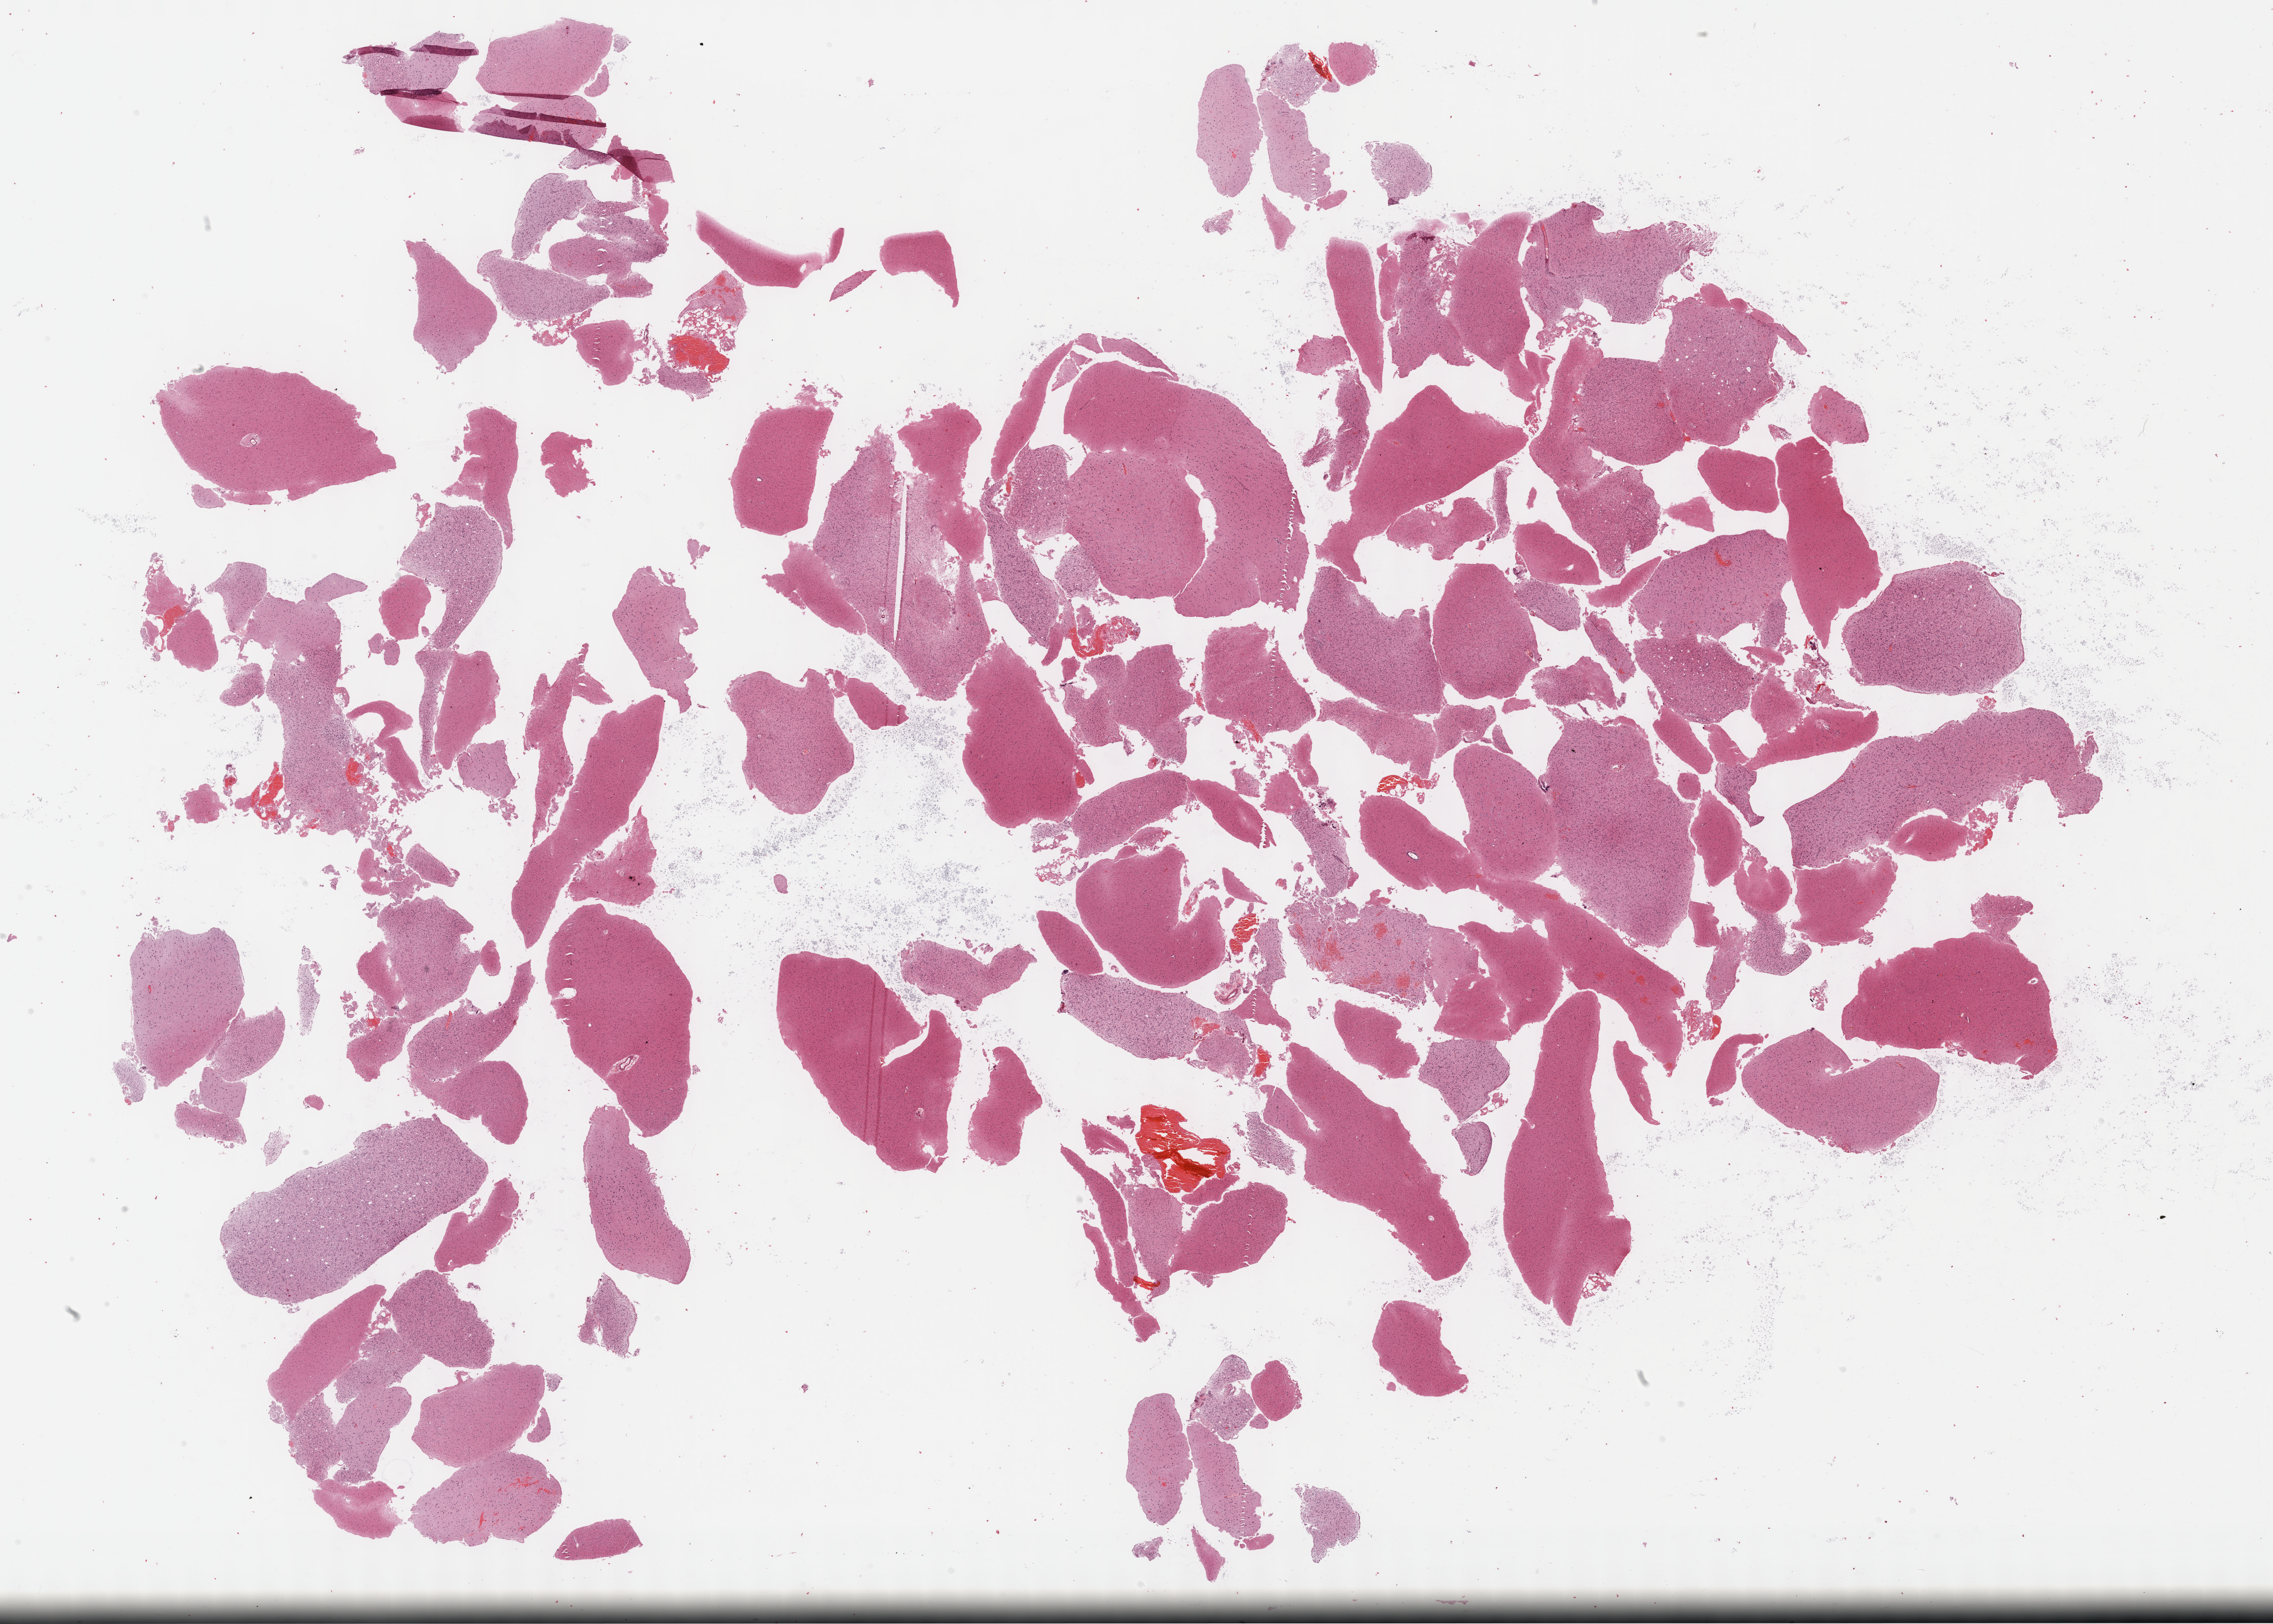
Whole-slide histology image, Hematoxylin and eosin (H&E) stained — low-resolution overview of the scanned area, about 32.2 x 23.0 mm; FFPE section; primary tumour sample from the brain. Male patient; age at initial diagnosis 19 years. Histologic grade: G2 (moderately differentiated).
Histologic diagnosis: Mixed glioma (cerebrum). Laterality: left.